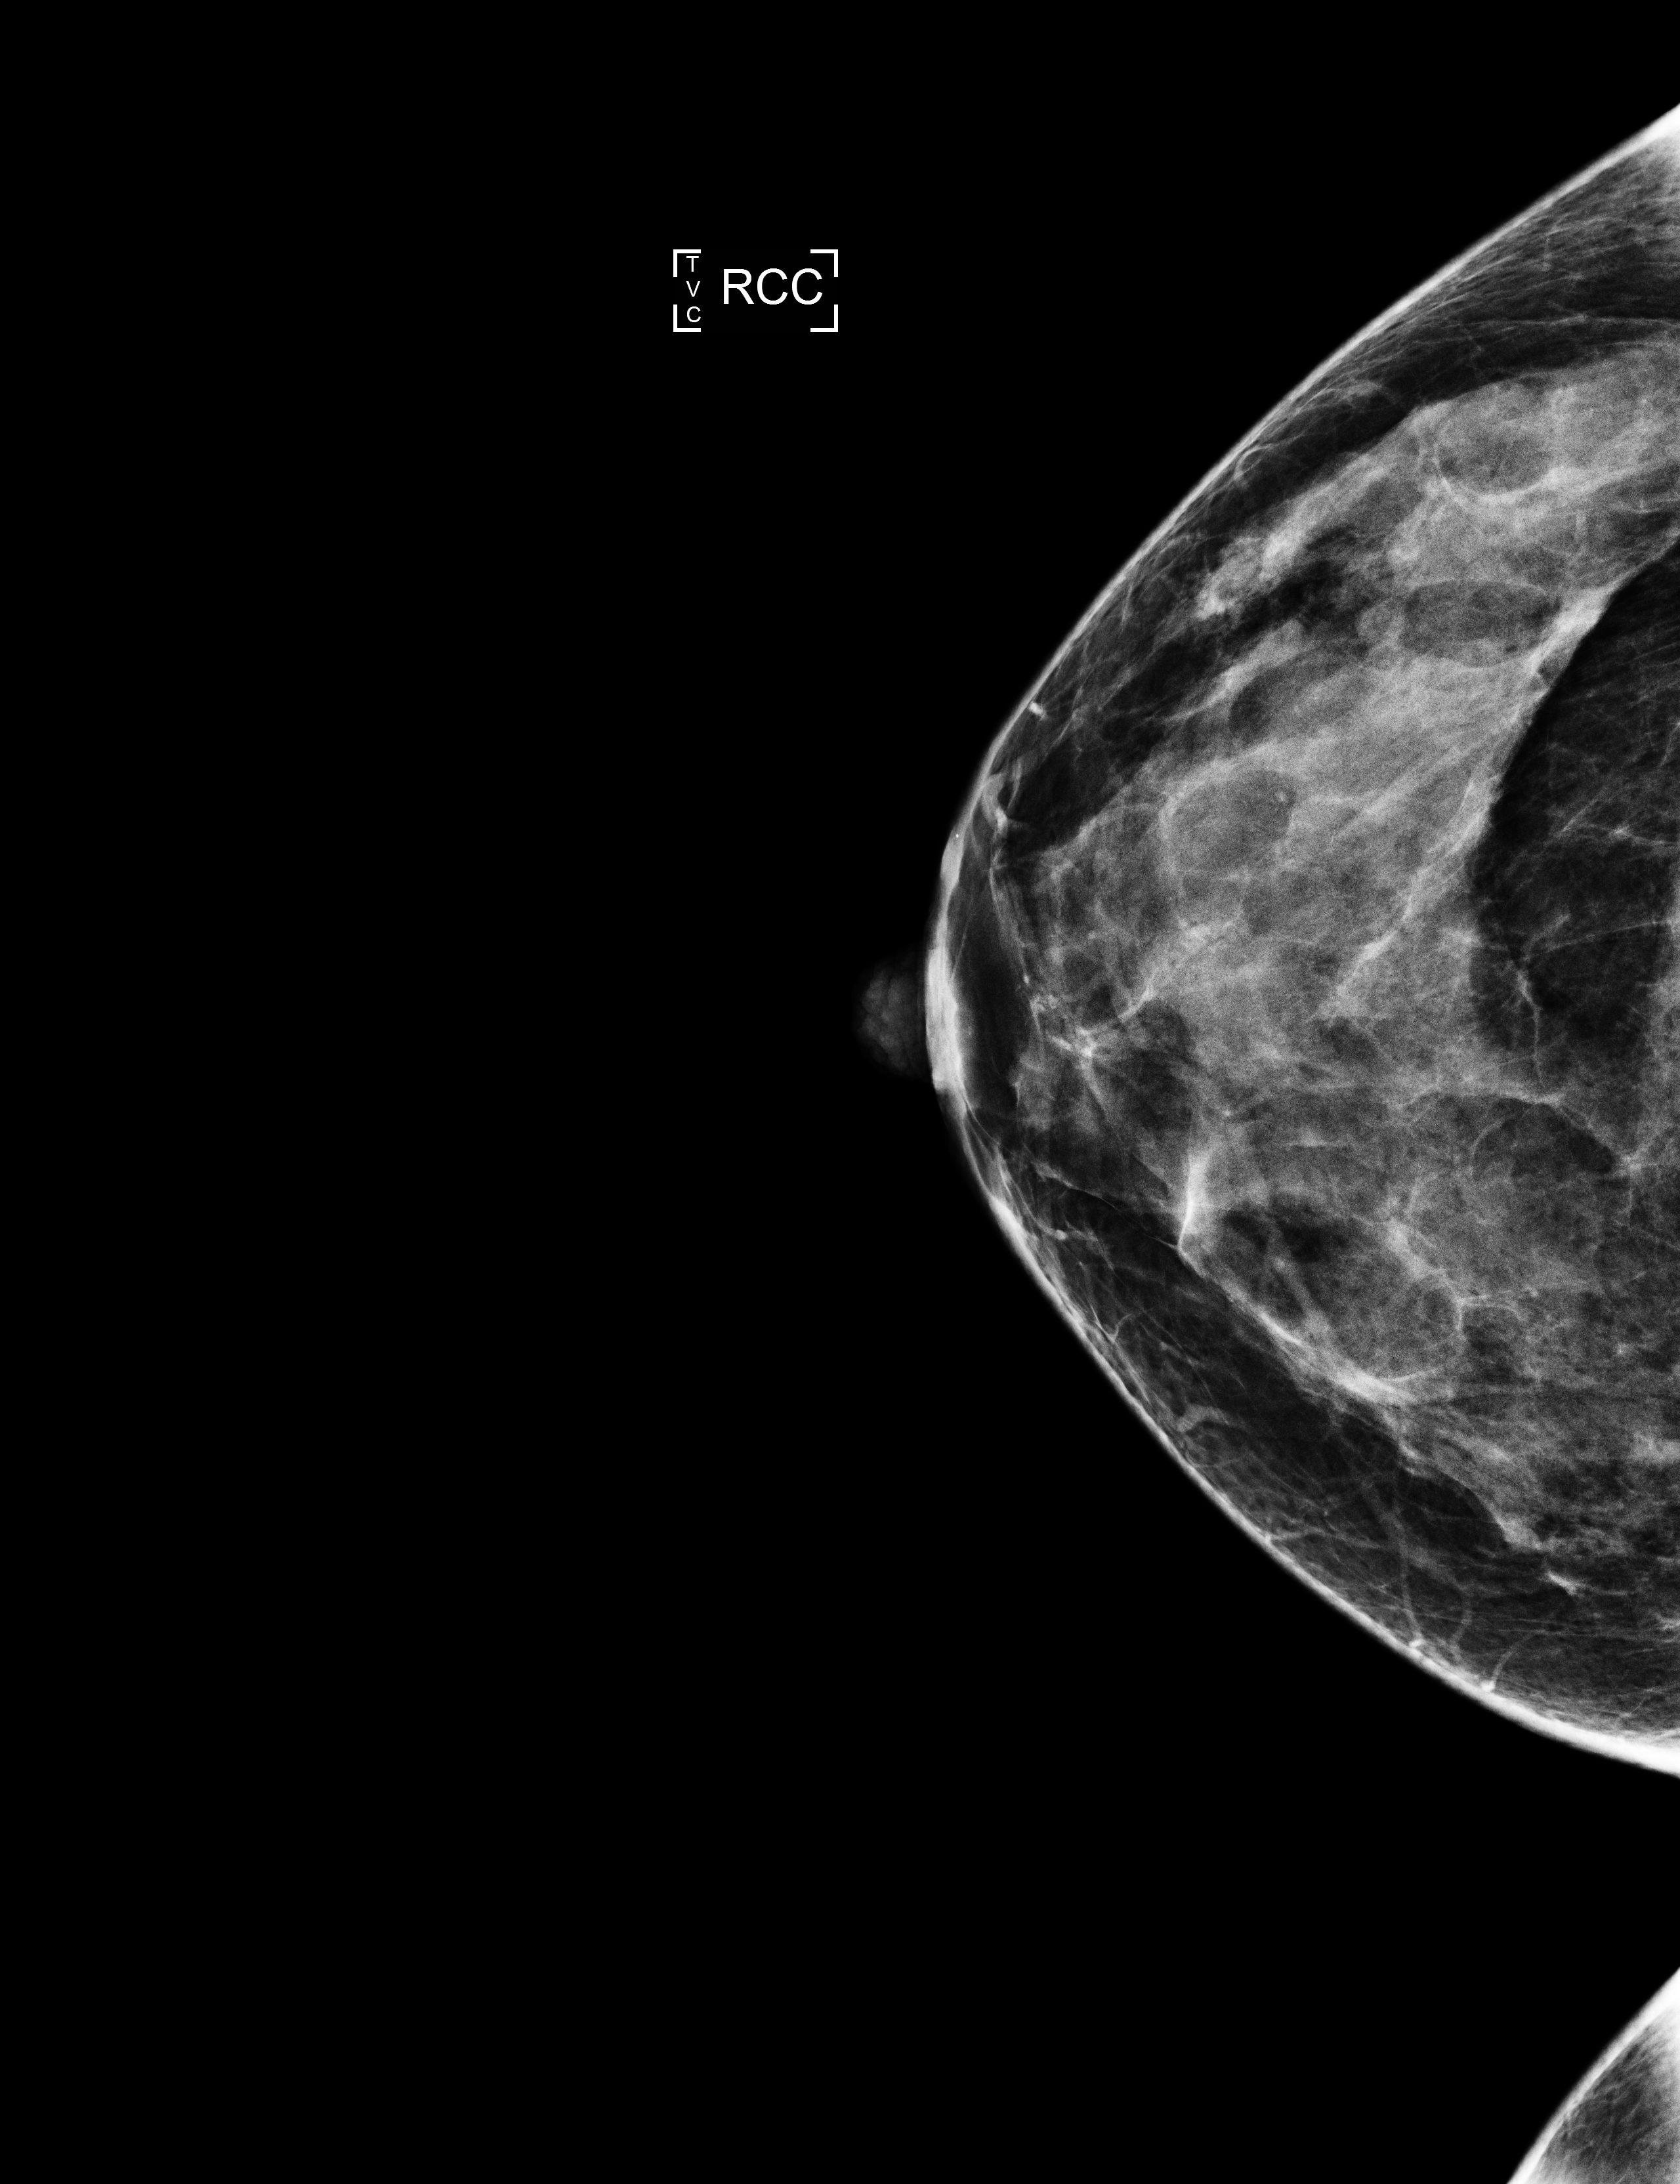
Screening examination. Patient: female, 50 years.
Image type: full-field digital mammogram. Breast: right. Projection: CC view.